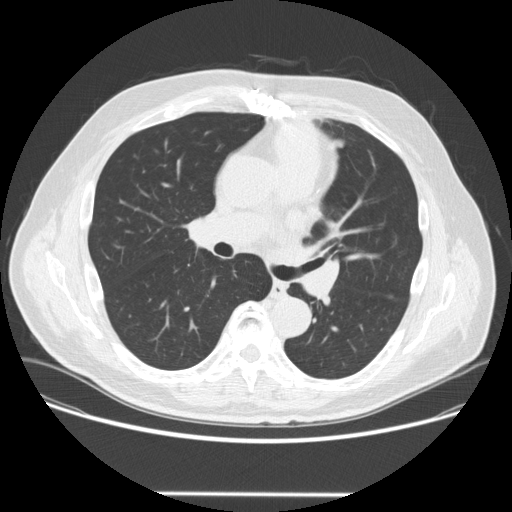
Low-dose screening chest CT, axial slice. Third screening round (two years after baseline). Lung window (W 1500 / L -600 HU). 120 kVp. 512 × 512 image matrix. Male, age 66 years at enrolment.
Expert-annotated lung lesion, bounding box <299,210,351,257> (left, top, right, bottom; pixels). The screening reader recorded 2 non-calcified nodules or masses ≥4 mm on this exam (left upper lobe, right lower lobe); which of them this box marks is not recorded. Official screen result: positive, other. Participant outcome: lung cancer diagnosed 85 days after this screen — squamous cell carcinoma, NOS, left upper lobe, poorly differentiated (G3), stage IA (AJCC 6th edition), 27 mm at pathology.